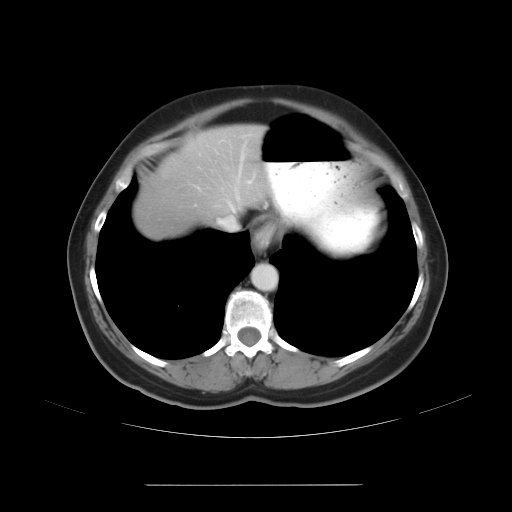
Contrast-enhanced abdominal CT, one axial slice; slice 24 of 27 in the series (ordered by position); 120 kVp; intravenous contrast given; soft-tissue window (W 400 / L 40 HU); 7.5 mm slice thickness; 512 × 512 image matrix, field of view 440 × 440 mm. Female patient, age 58 years. Case-level facts recorded for this patient, not image findings: diagnosis: colorectal cancer liver metastases, imaged before liver resection; multiple liver metastases: yes; largest metastasis: 1.9 cm; chemotherapy before resection: yes.
Structures marked on this image (outlined manually by an expert reader):
- hepatic veins: bounding box [x1, y1, x2, y2] px = [218, 145, 245, 230]
- liver: [140, 126, 268, 228]
- planned liver remnant (the part of the liver to remain after resection): [140, 127, 267, 221]